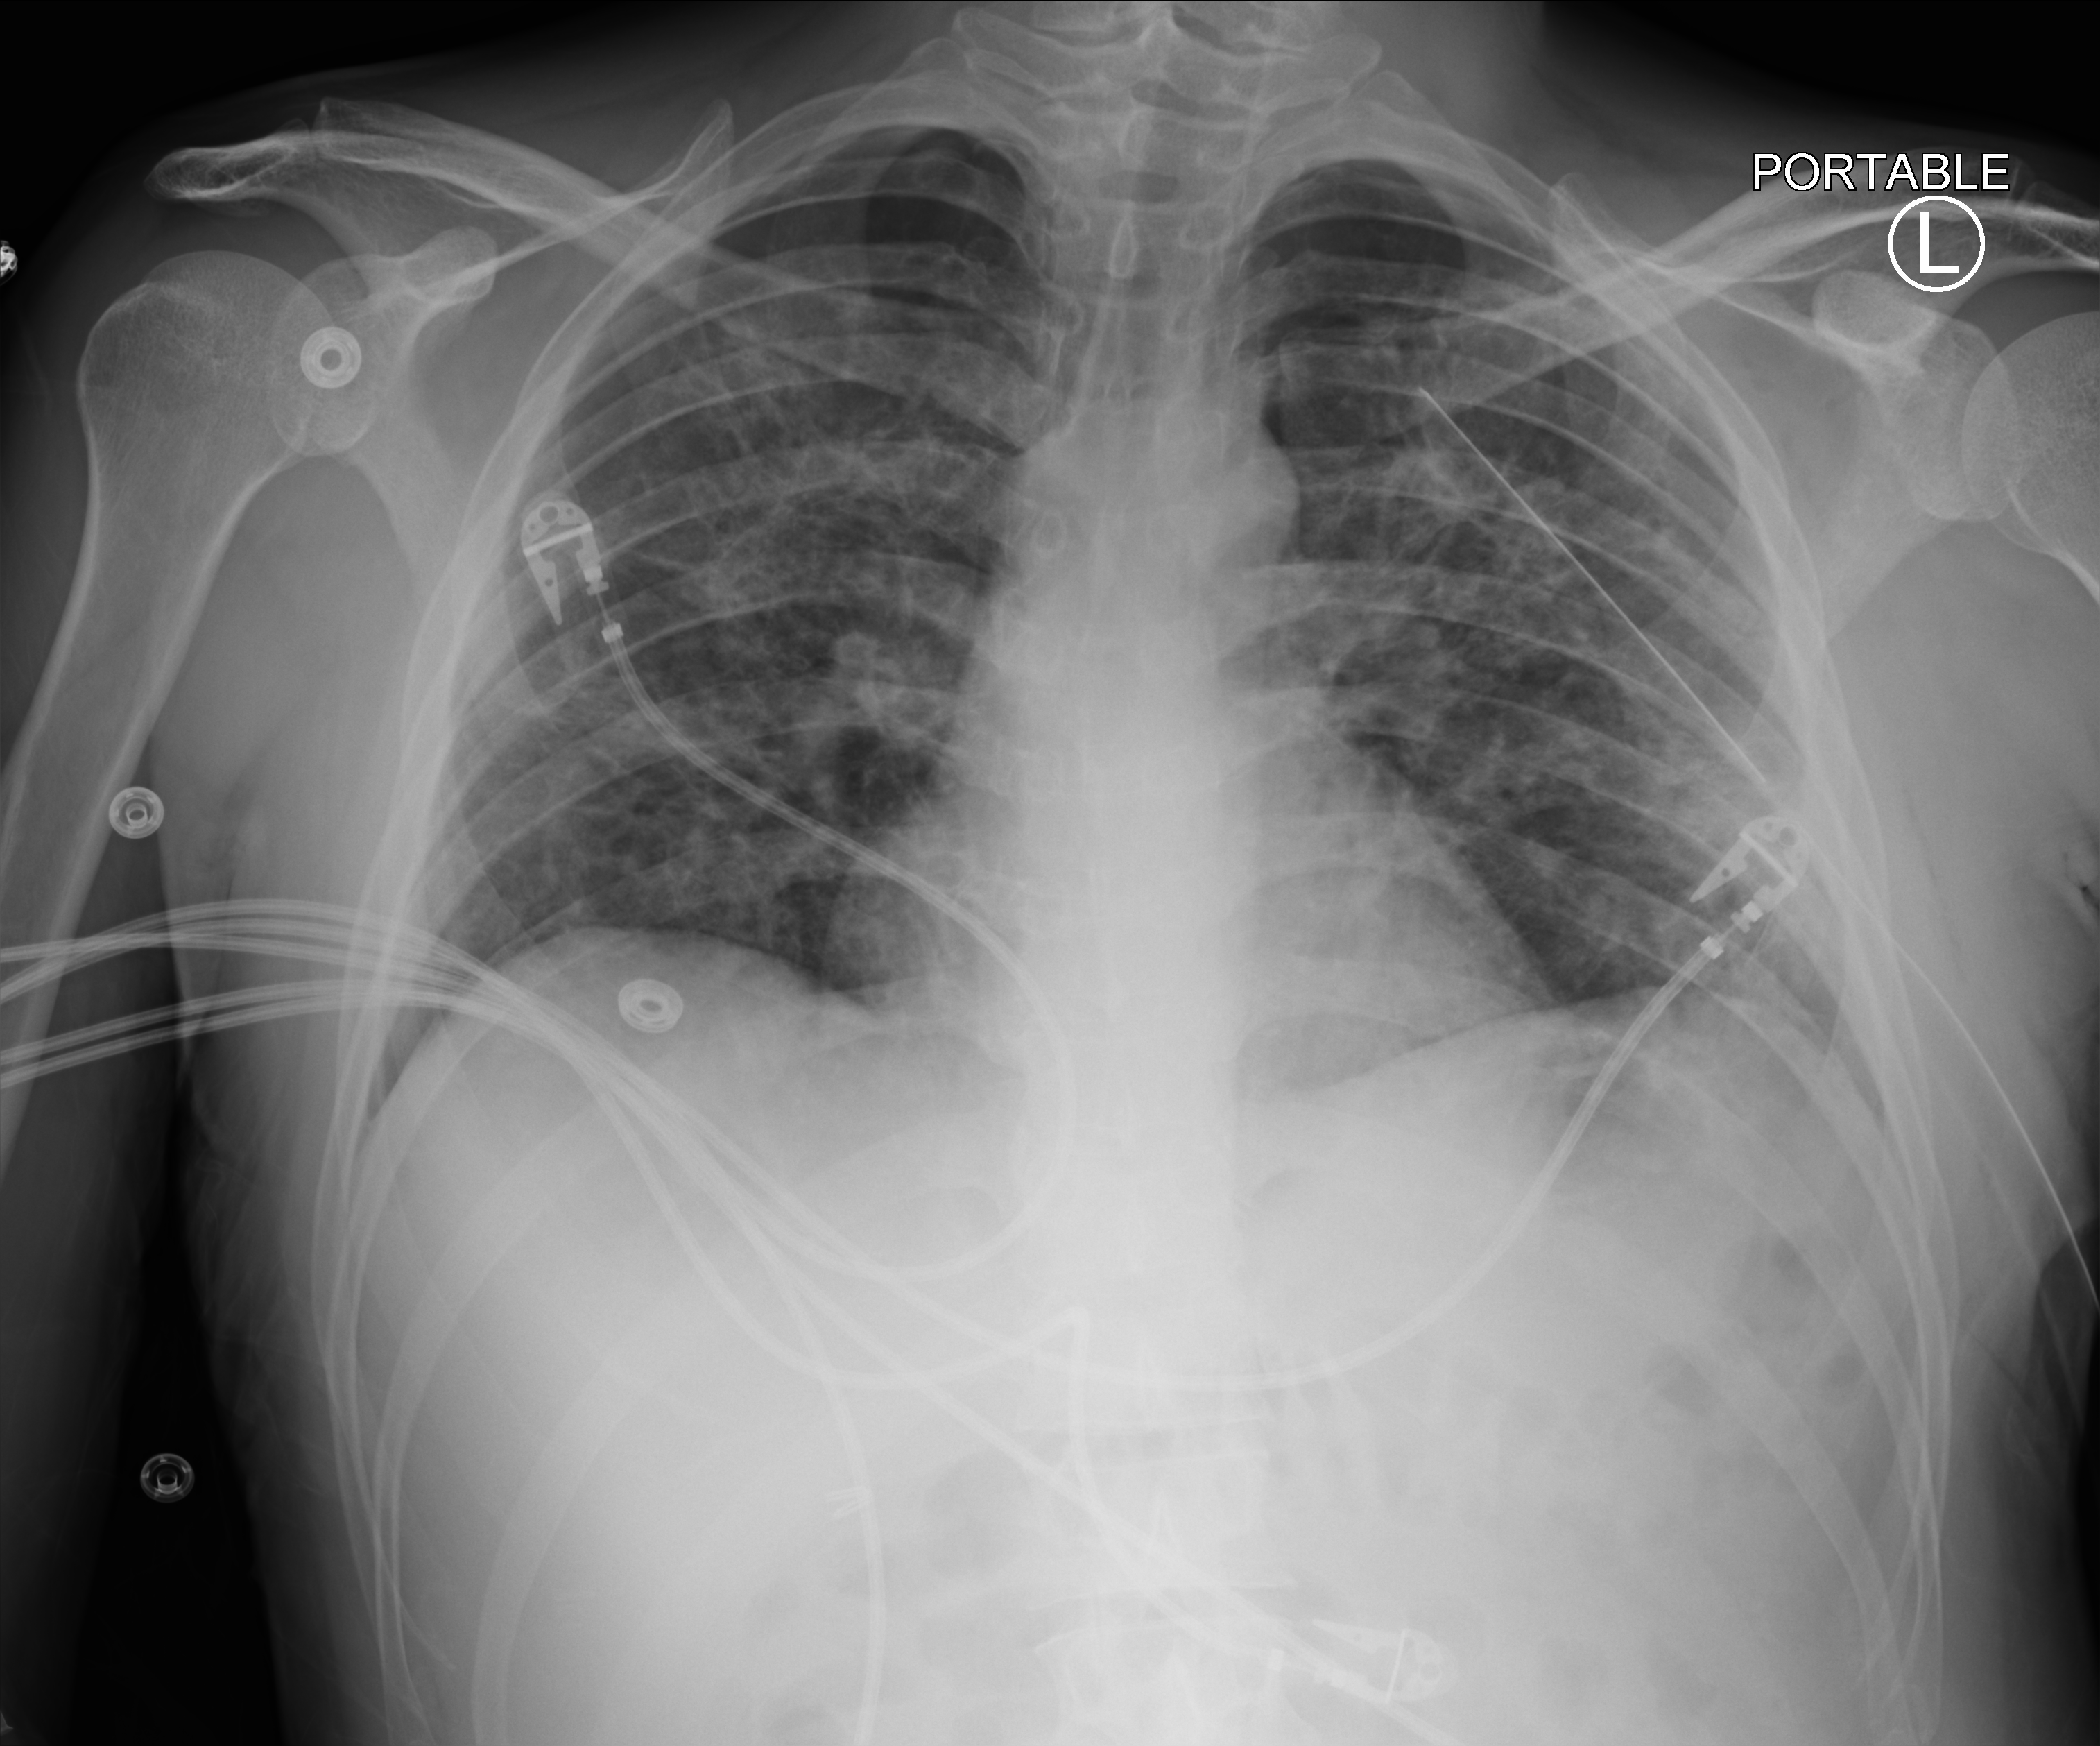
Bedside chest radiograph (computed radiography); anteroposterior (AP) projection. Patient hospitalised with COVID-19; male, aged 18–59 years.
From the hospital-stay record, not from the radiograph (when in the stay this image was taken is not recorded): hypertension (admission record): no; COPD (admission record): no; mechanically ventilated during this hospital stay: yes.